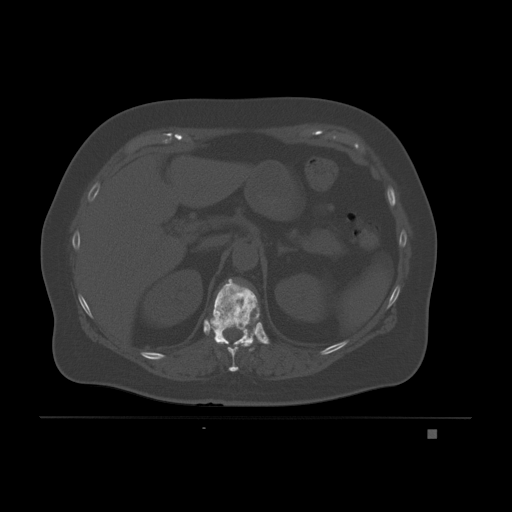
CT including the spine, one axial slice; slice 92 of 221 in the series (ordered by position); bone window (W 1800 / L 400 HU); 512 × 512 image matrix, field of view 474 × 474 mm. Patient: female, 63 years. From the clinical record (not read from this slice): primary cancer: breast.
Outlined on this slice (semi-automatically segmented with operator editing):
- T10 vertebra: bounding box <227,343,254,372> (left, top, right, bottom; pixels)
- T11 vertebra: <211,278,260,347>